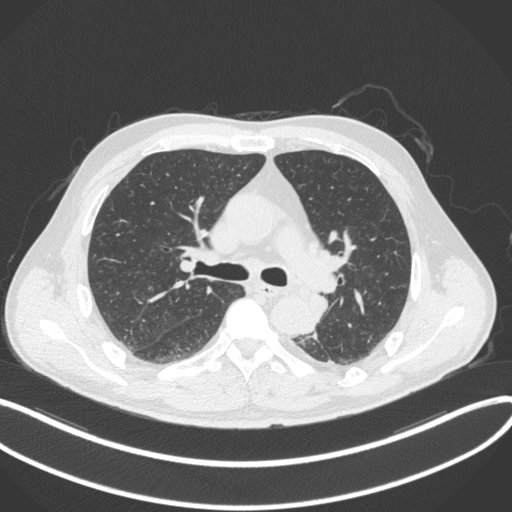
Chest CT, one axial slice; position 219 of 328 along the scan axis; reconstruction kernel B31f; lung window (W 1500 / L -600 HU); 1 mm slice thickness; 512 × 512 image matrix. Male patient, age 59 years. Case-level facts recorded for this patient, not image findings: clinical TNM (as recorded): T2a N2 M0.
Outlined on this slice (bounding box drawn by a radiologist):
- lung tumour (recorded histology: squamous cell carcinoma): bounding box (x1, y1, x2, y2) in pixels: (307, 293, 333, 327)